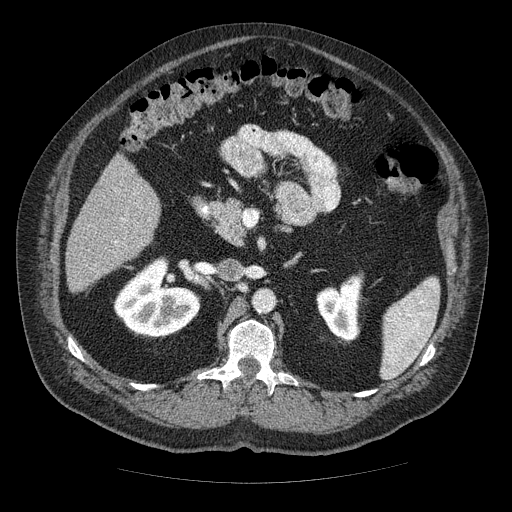
Contrast-enhanced abdominal CT (liver protocol), one axial slice. Position 20 of 85 along the scan axis. Reconstruction kernel STANDARD. 120 kVp. Soft-tissue window (W 400 / L 40 HU). 2.5 mm slice thickness. 512 × 512 image matrix. From the clinical record (not read from this slice): diagnosis: hepatocellular carcinoma (patient treated with transarterial chemoembolisation; whether this scan precedes or follows treatment is not stated here); TNM stage (as recorded): Stage-IIIA; Child-Pugh class: A; tumour nodularity: multinodular.
Structures marked on this image (semi-automatic segmentation, software-assisted and operator-edited):
- liver parenchyma outside the tumour (the mass and vessels are separate outlines, so this box may not span the whole liver): bounding box <66,154,160,292> (left, top, right, bottom; pixels)
- liver vessels: <115,218,125,243>